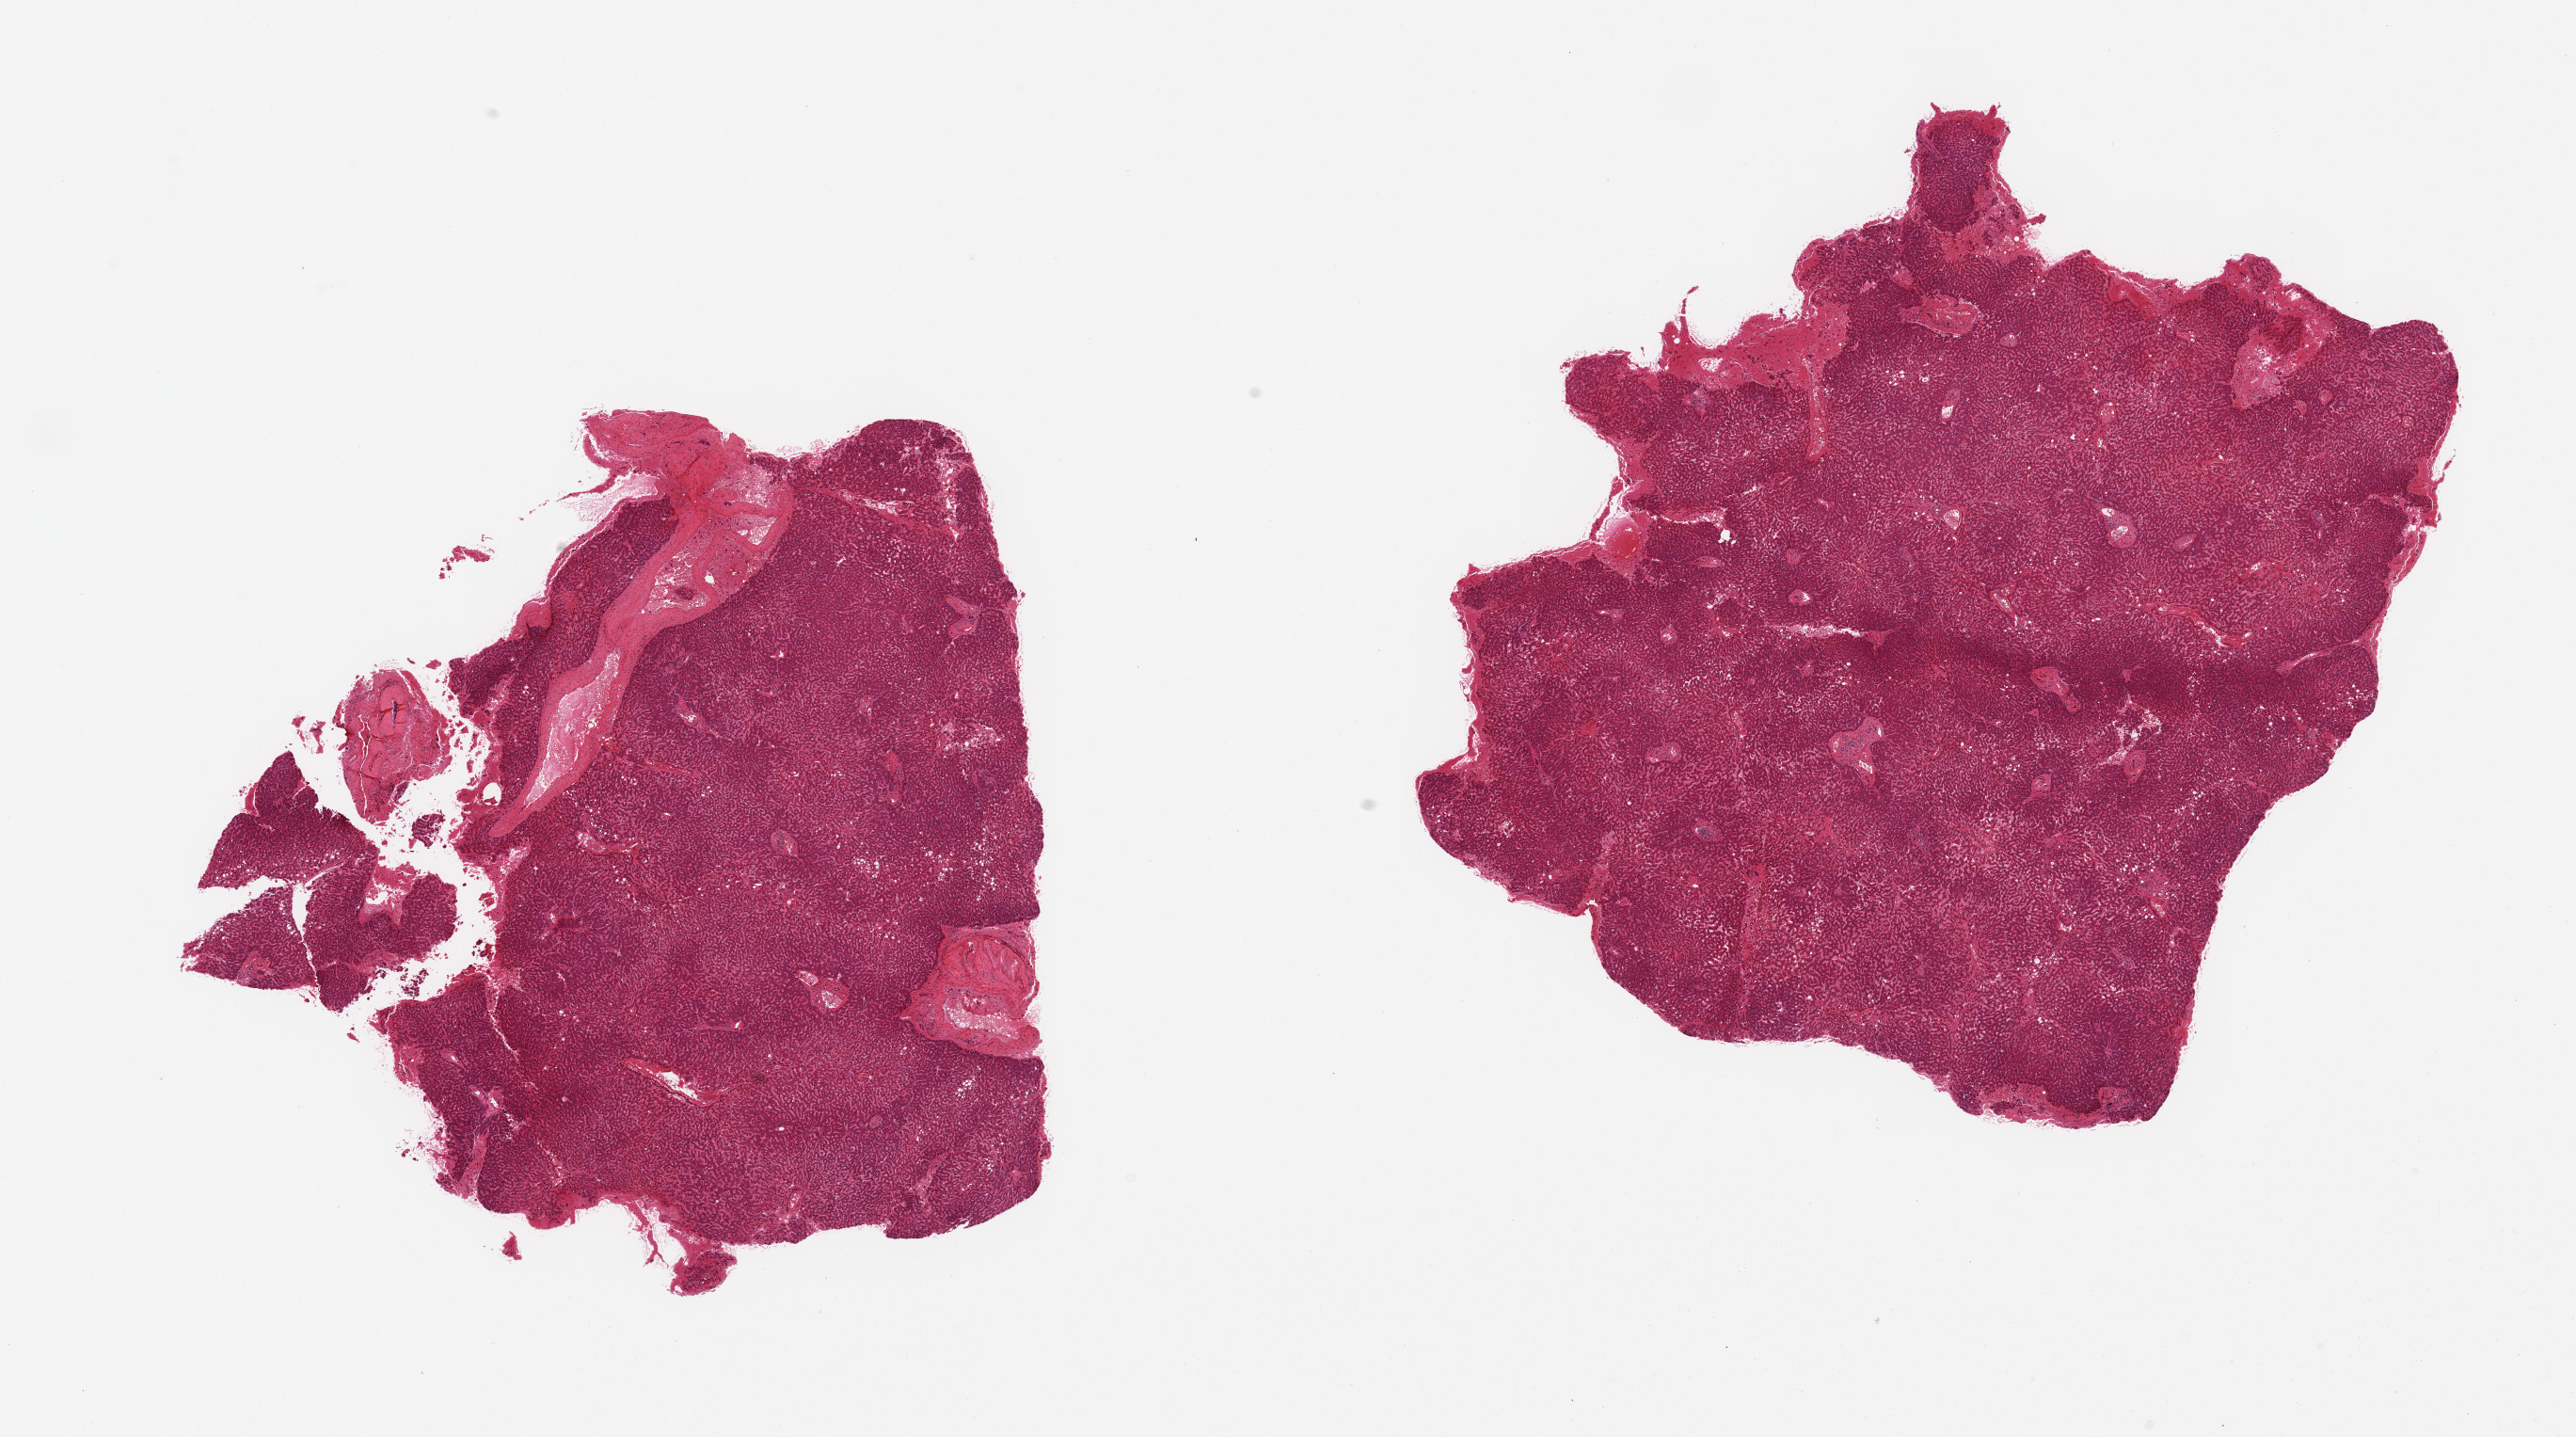
Hematoxylin and eosin (H&E) whole-slide image, brightfield — low-resolution overview of the scanned area, about 21.7 x 12.1 mm; PAXgene-fixed, paraffin-embedded tissue; sampled site (target tissue): liver; tissue donor sample.
Pathologist's review note for this sample: 2 pieces; central congestion.